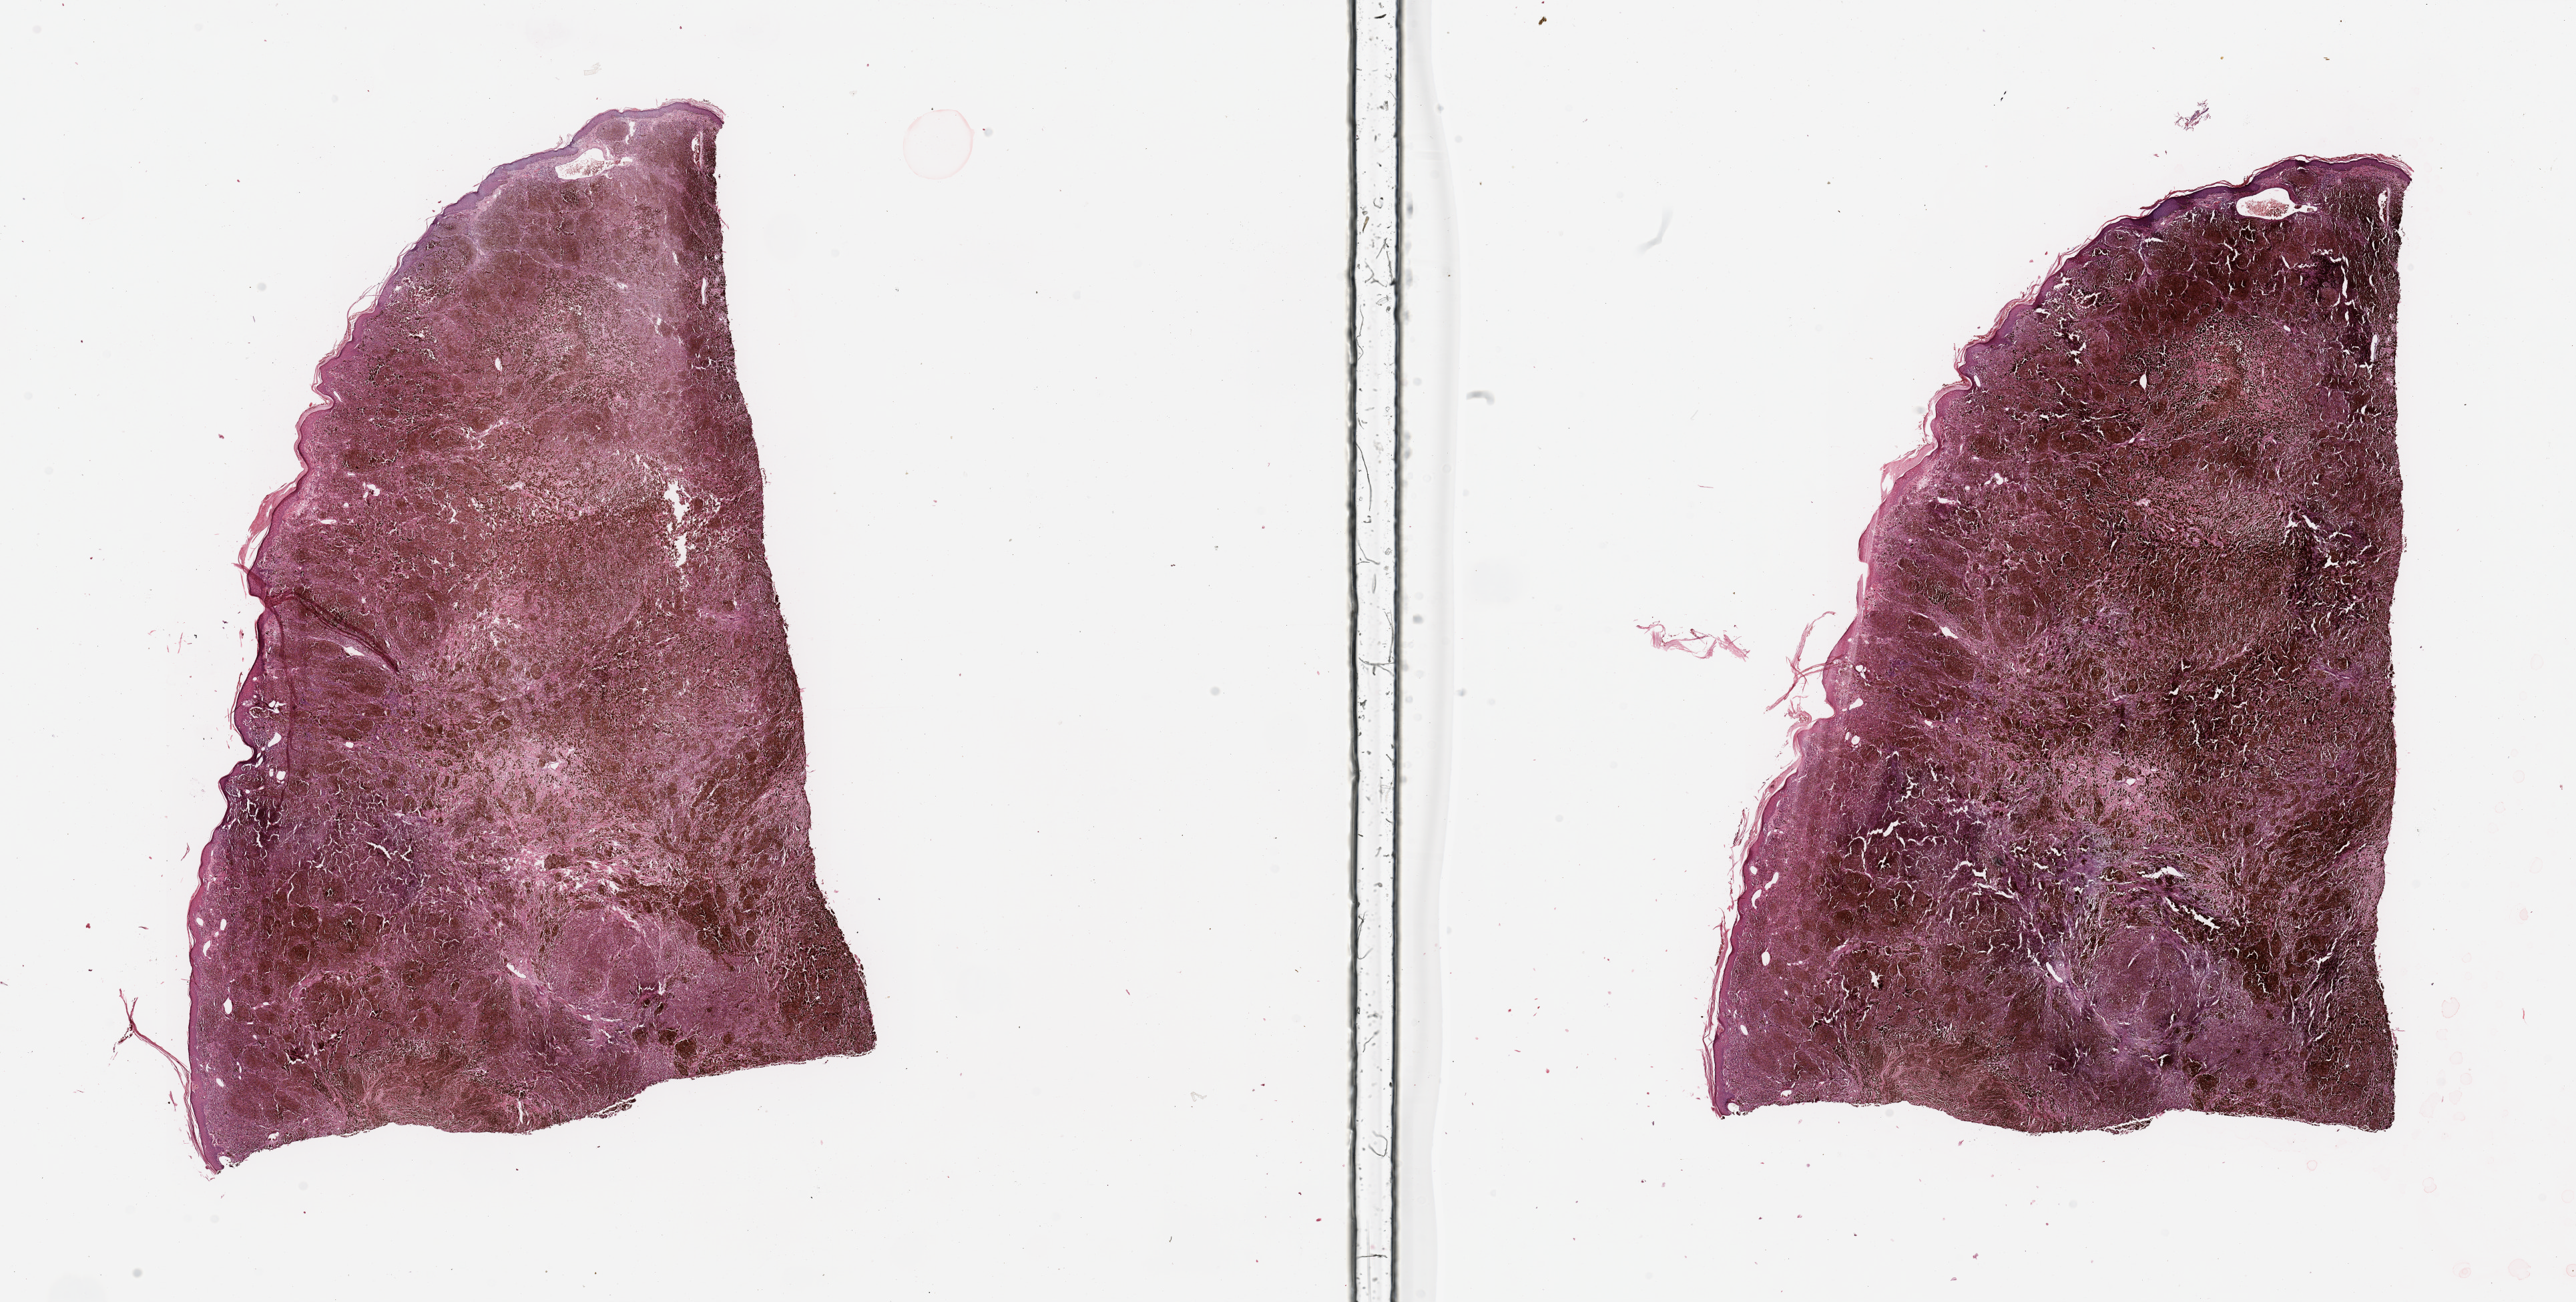
Digitized Hematoxylin and eosin (H&E) stained tissue section (whole slide) — a low-resolution overview of the entire scanned area, about 30.5 x 15.4 mm (from a 20x scan). Melanoma tumour tissue; sampled site not recorded. 66-year-old male patient.
AJCC pathologic stage: IV. Diagnosis: Malignant melanoma, NOS. Primary tumour site (as recorded): trunk.